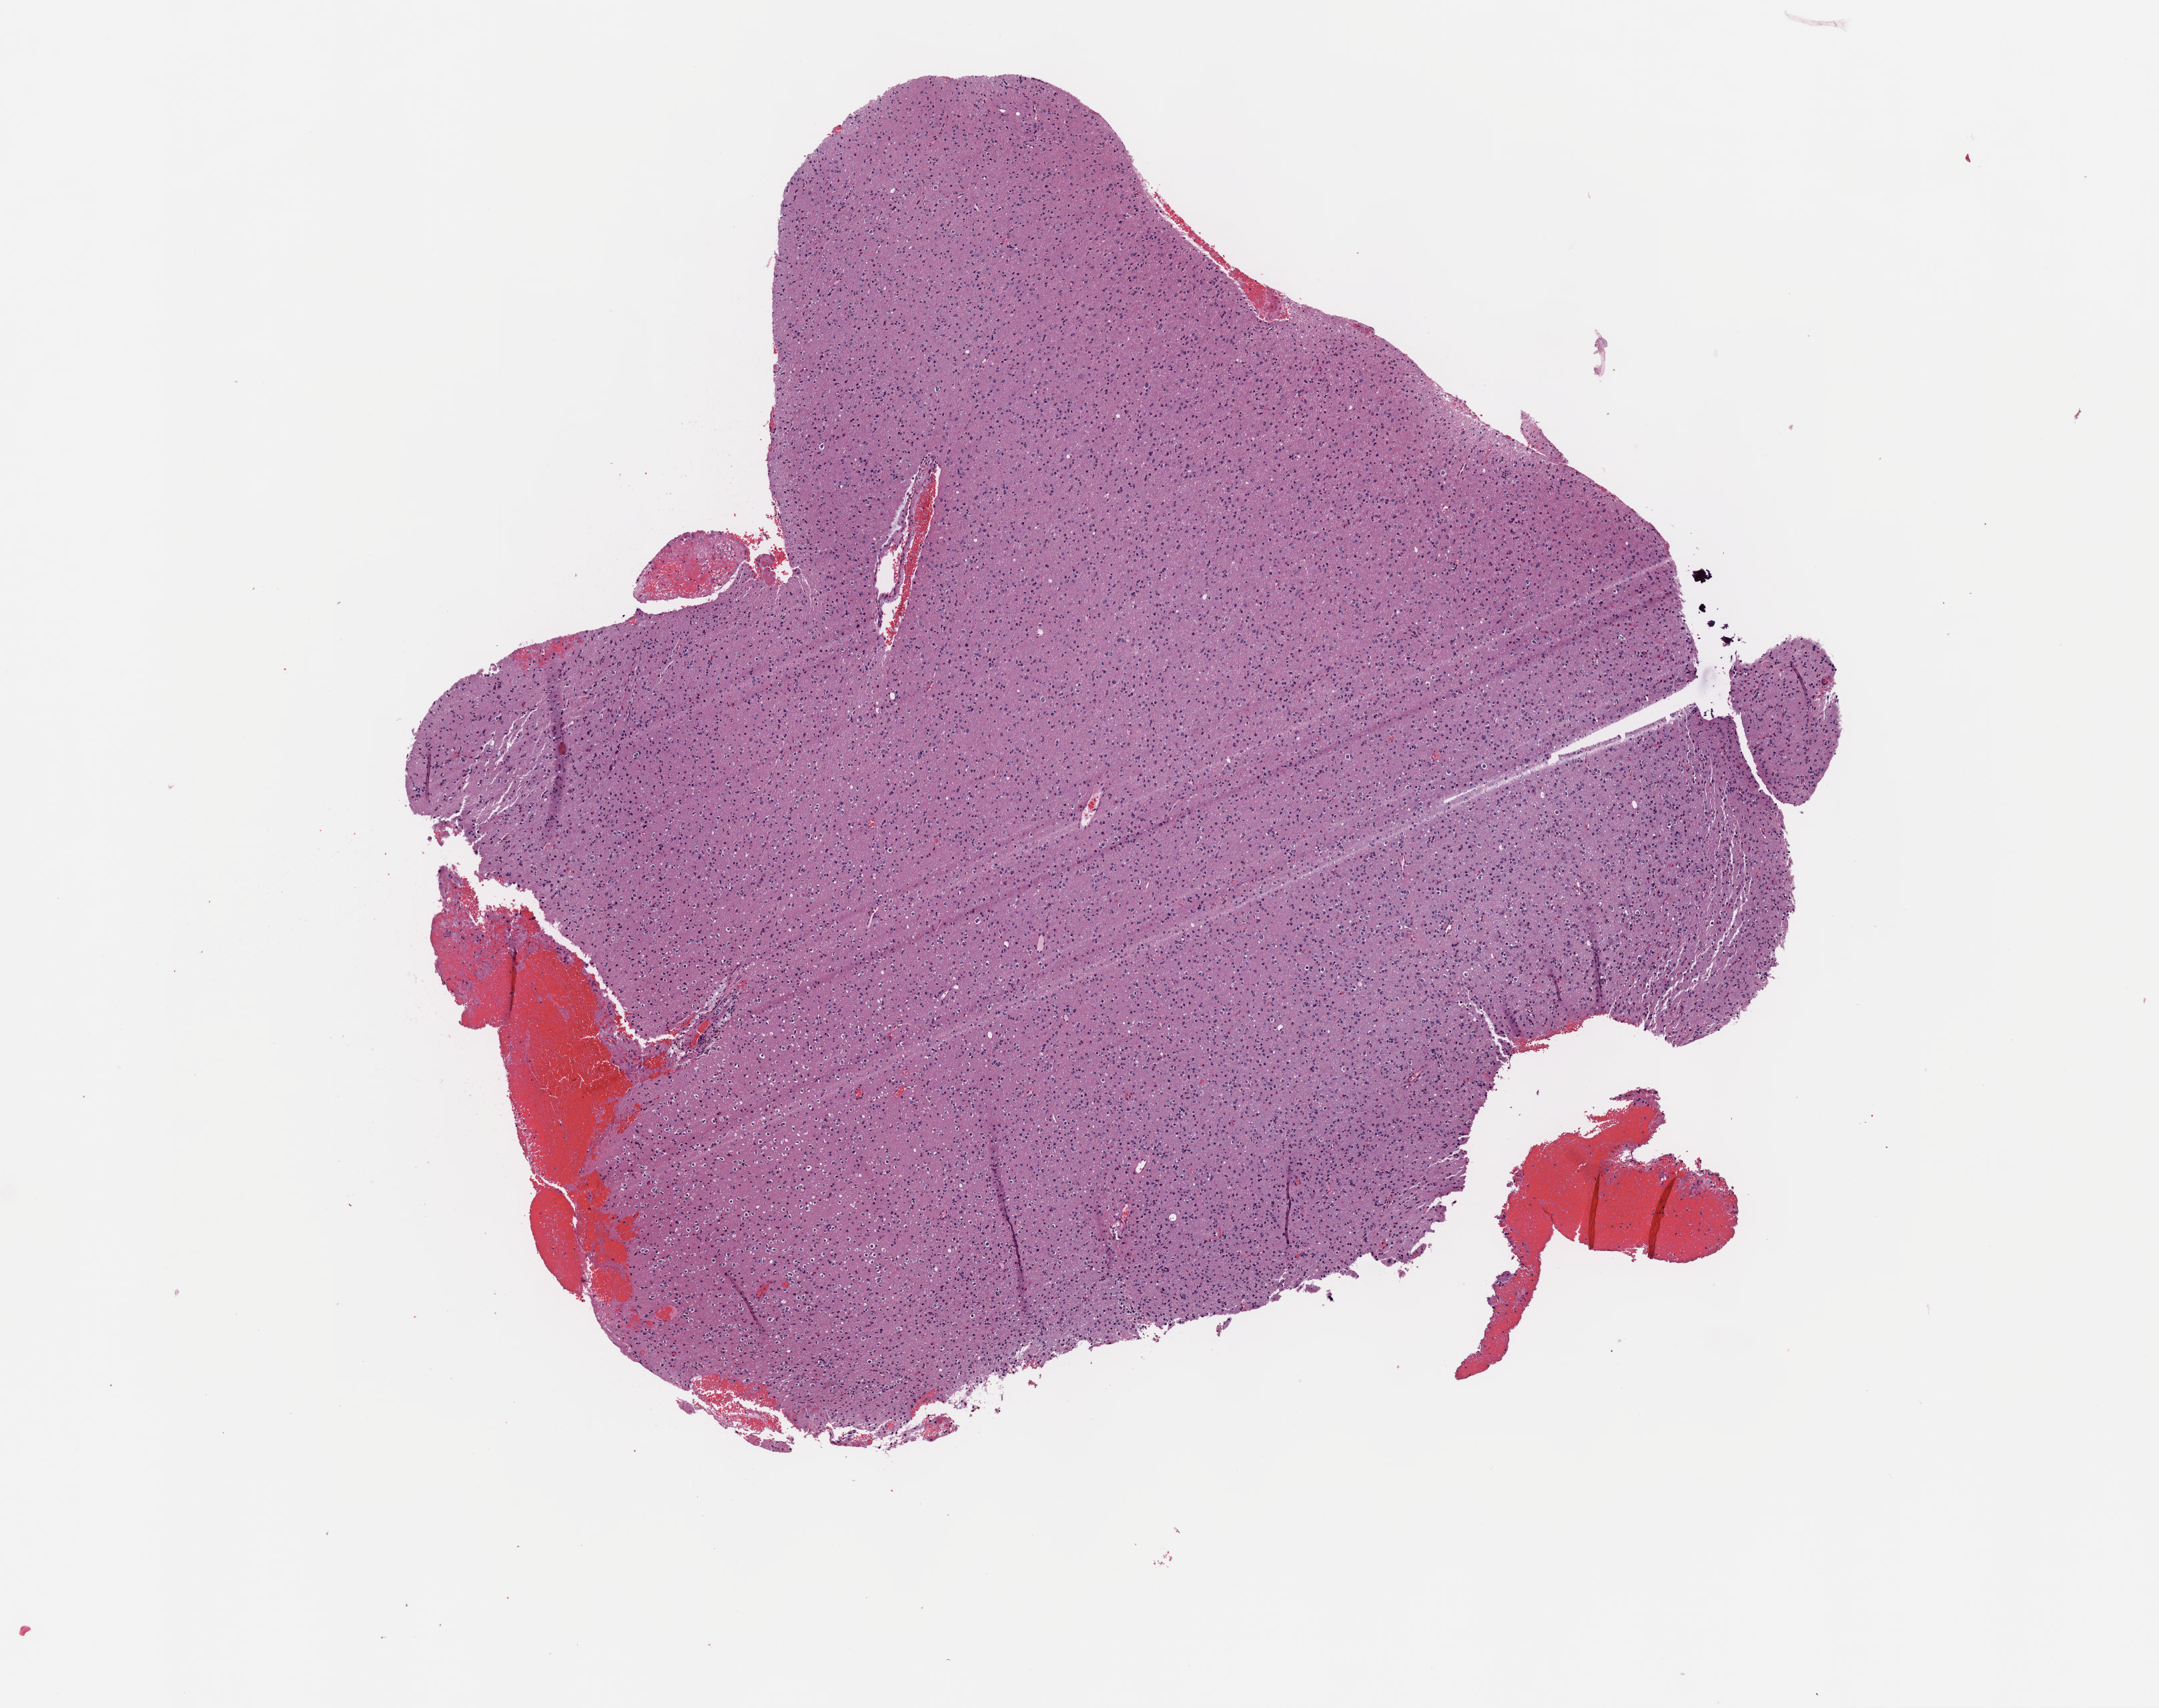
Whole-slide histology image, Hematoxylin and eosin (H&E) stained, low-resolution overview of the scanned area, about 6.5 x 5.2 mm (from a 40x scan); formalin-fixed paraffin-embedded (FFPE) diagnostic section; primary tumour sample from the brain. Patient: male, age at initial diagnosis 52 years. Histologic grade: G2 (moderately differentiated).
• laterality: right
• diagnosis: Mixed glioma (cerebrum)